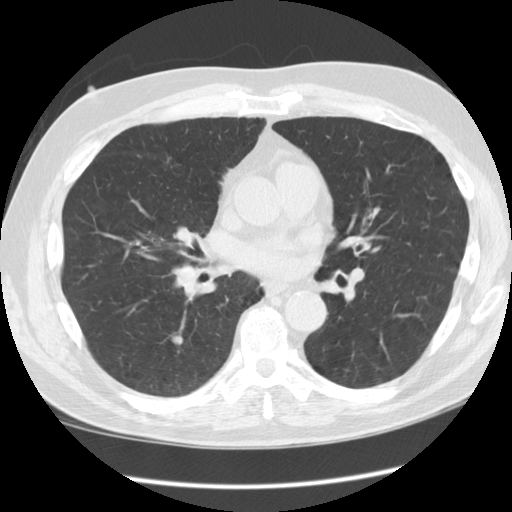
Chest CT (low-dose screening protocol), one axial image; third screening round (two years after baseline); lung window (W 1500 / L -600 HU); standard (soft-tissue) reconstruction kernel (STANDARD); 120 kVp; slice 65 of 128 in the series. Male, age 60 years at enrolment. Former smoker at enrolment.
Lesion marked by an expert reader, box from (x=152, y=328) to (x=191, y=358) px. The screening reader recorded 5 non-calcified nodules or masses ≥4 mm on this exam (right middle lobe, right upper lobe, left upper lobe, left lower lobe, right upper lobe); which of them this box marks is not recorded. Official screen result: positive, other. Lung cancer was diagnosed 353 days after this screen: squamous cell carcinoma, clear cell type, right lower lobe, stage IV (AJCC 6th edition), 12 mm at pathology.